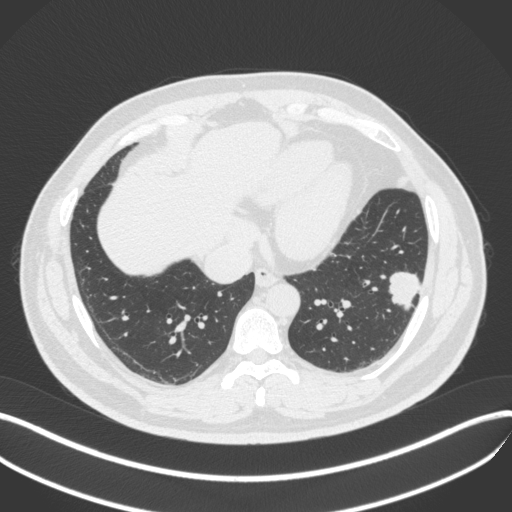
Chest CT, one axial slice. Position 136 of 420 along the scan axis. Reconstruction kernel B31f. 120 kVp. Lung window (W 1500 / L -600 HU). 1 mm slice thickness. 512 × 512 image matrix, field of view 400 × 400 mm. Male patient, age 39 years. From the clinical record (not read from this slice): clinical TNM (as recorded): T2a N0 M0; histopathological grade: G2-3.
Structures marked on this image (bounding box drawn by a radiologist):
- lung tumour (recorded histology: adenocarcinoma): bounding box [x1, y1, x2, y2] px = [383, 267, 425, 311]